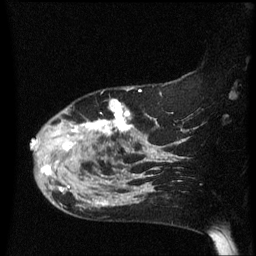
Breast MRI (dynamic contrast-enhanced), one sagittal slice; dynamic contrast-enhanced series, image 2 of 3 at this slice position (ordered by acquisition); 1.5 T; TE 4.2 ms, TR 8.4 ms; 2.2 mm slice thickness; 256 × 256 image matrix. Female patient, age 47 years.
Structures marked on this image (semi-automatically segmented with operator editing):
- analysis volume of interest (the breast-tissue region the enhancement analysis was run in; not a lesion): bounding box <32,100,149,206> (left, top, right, bottom; pixels)
- tumour enhancement mask (voxels above the 70 % enhancement threshold inside the analysis volume of interest): <32,100,149,205>